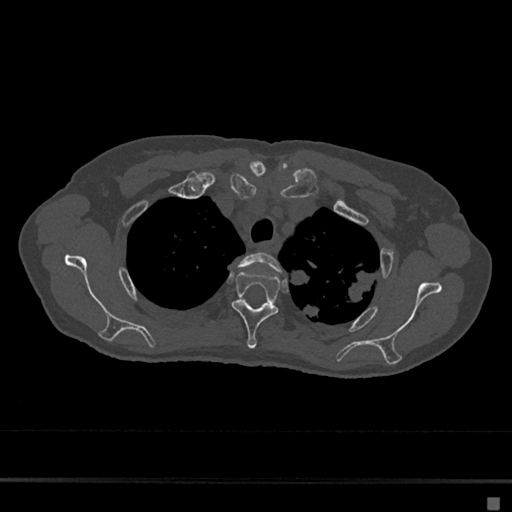
CT including the spine, one axial slice; position 539 of 797 along the scan axis; 120 kVp; bone window (W 1800 / L 400 HU); 0.5 mm slice thickness; 512 × 512 image matrix, field of view 360 × 360 mm. Patient: female, 68 years. From the clinical record (not read from this slice): primary cancer: renal.
Structures marked on this image (semi-automatic segmentation, software-assisted and operator-edited):
- T2 vertebra: bounding box (x1, y1, x2, y2) in pixels: (238, 252, 281, 272)
- T3 vertebra: (232, 271, 280, 349)